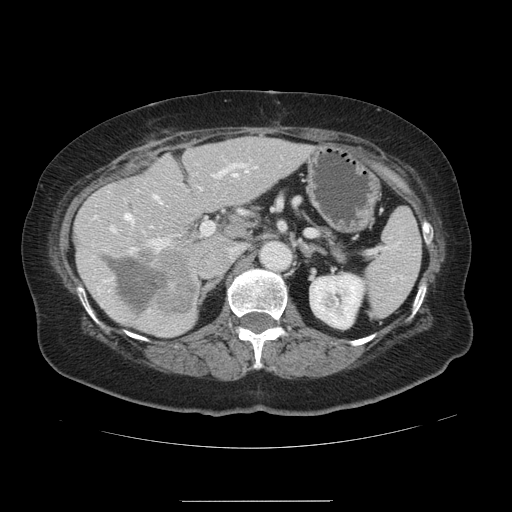
Contrast-enhanced abdominal CT, one axial slice. Position 73 of 141 along the scan axis. Intravenous contrast given. Soft-tissue window (W 400 / L 40 HU). 512 × 512 image matrix, field of view 393 × 393 mm. Female patient, age 74 years. Case-level facts recorded for this patient, not image findings: diagnosis: colorectal cancer liver metastases, imaged before liver resection; multiple liver metastases: yes; largest metastasis: 7 cm; disease in both lobes: yes.
Structures marked on this image (outlined manually by an expert reader):
- hepatic veins: box from (x=125, y=173) to (x=237, y=229) px
- liver: (x=75, y=137)–(x=308, y=336)
- planned liver remnant (the part of the liver to remain after resection): (x=80, y=137)–(x=308, y=336)
- portal vein (with intrahepatic branches): (x=110, y=163)–(x=248, y=254)
- liver metastasis: (x=109, y=260)–(x=168, y=313)
- liver metastasis: (x=138, y=252)–(x=194, y=313)